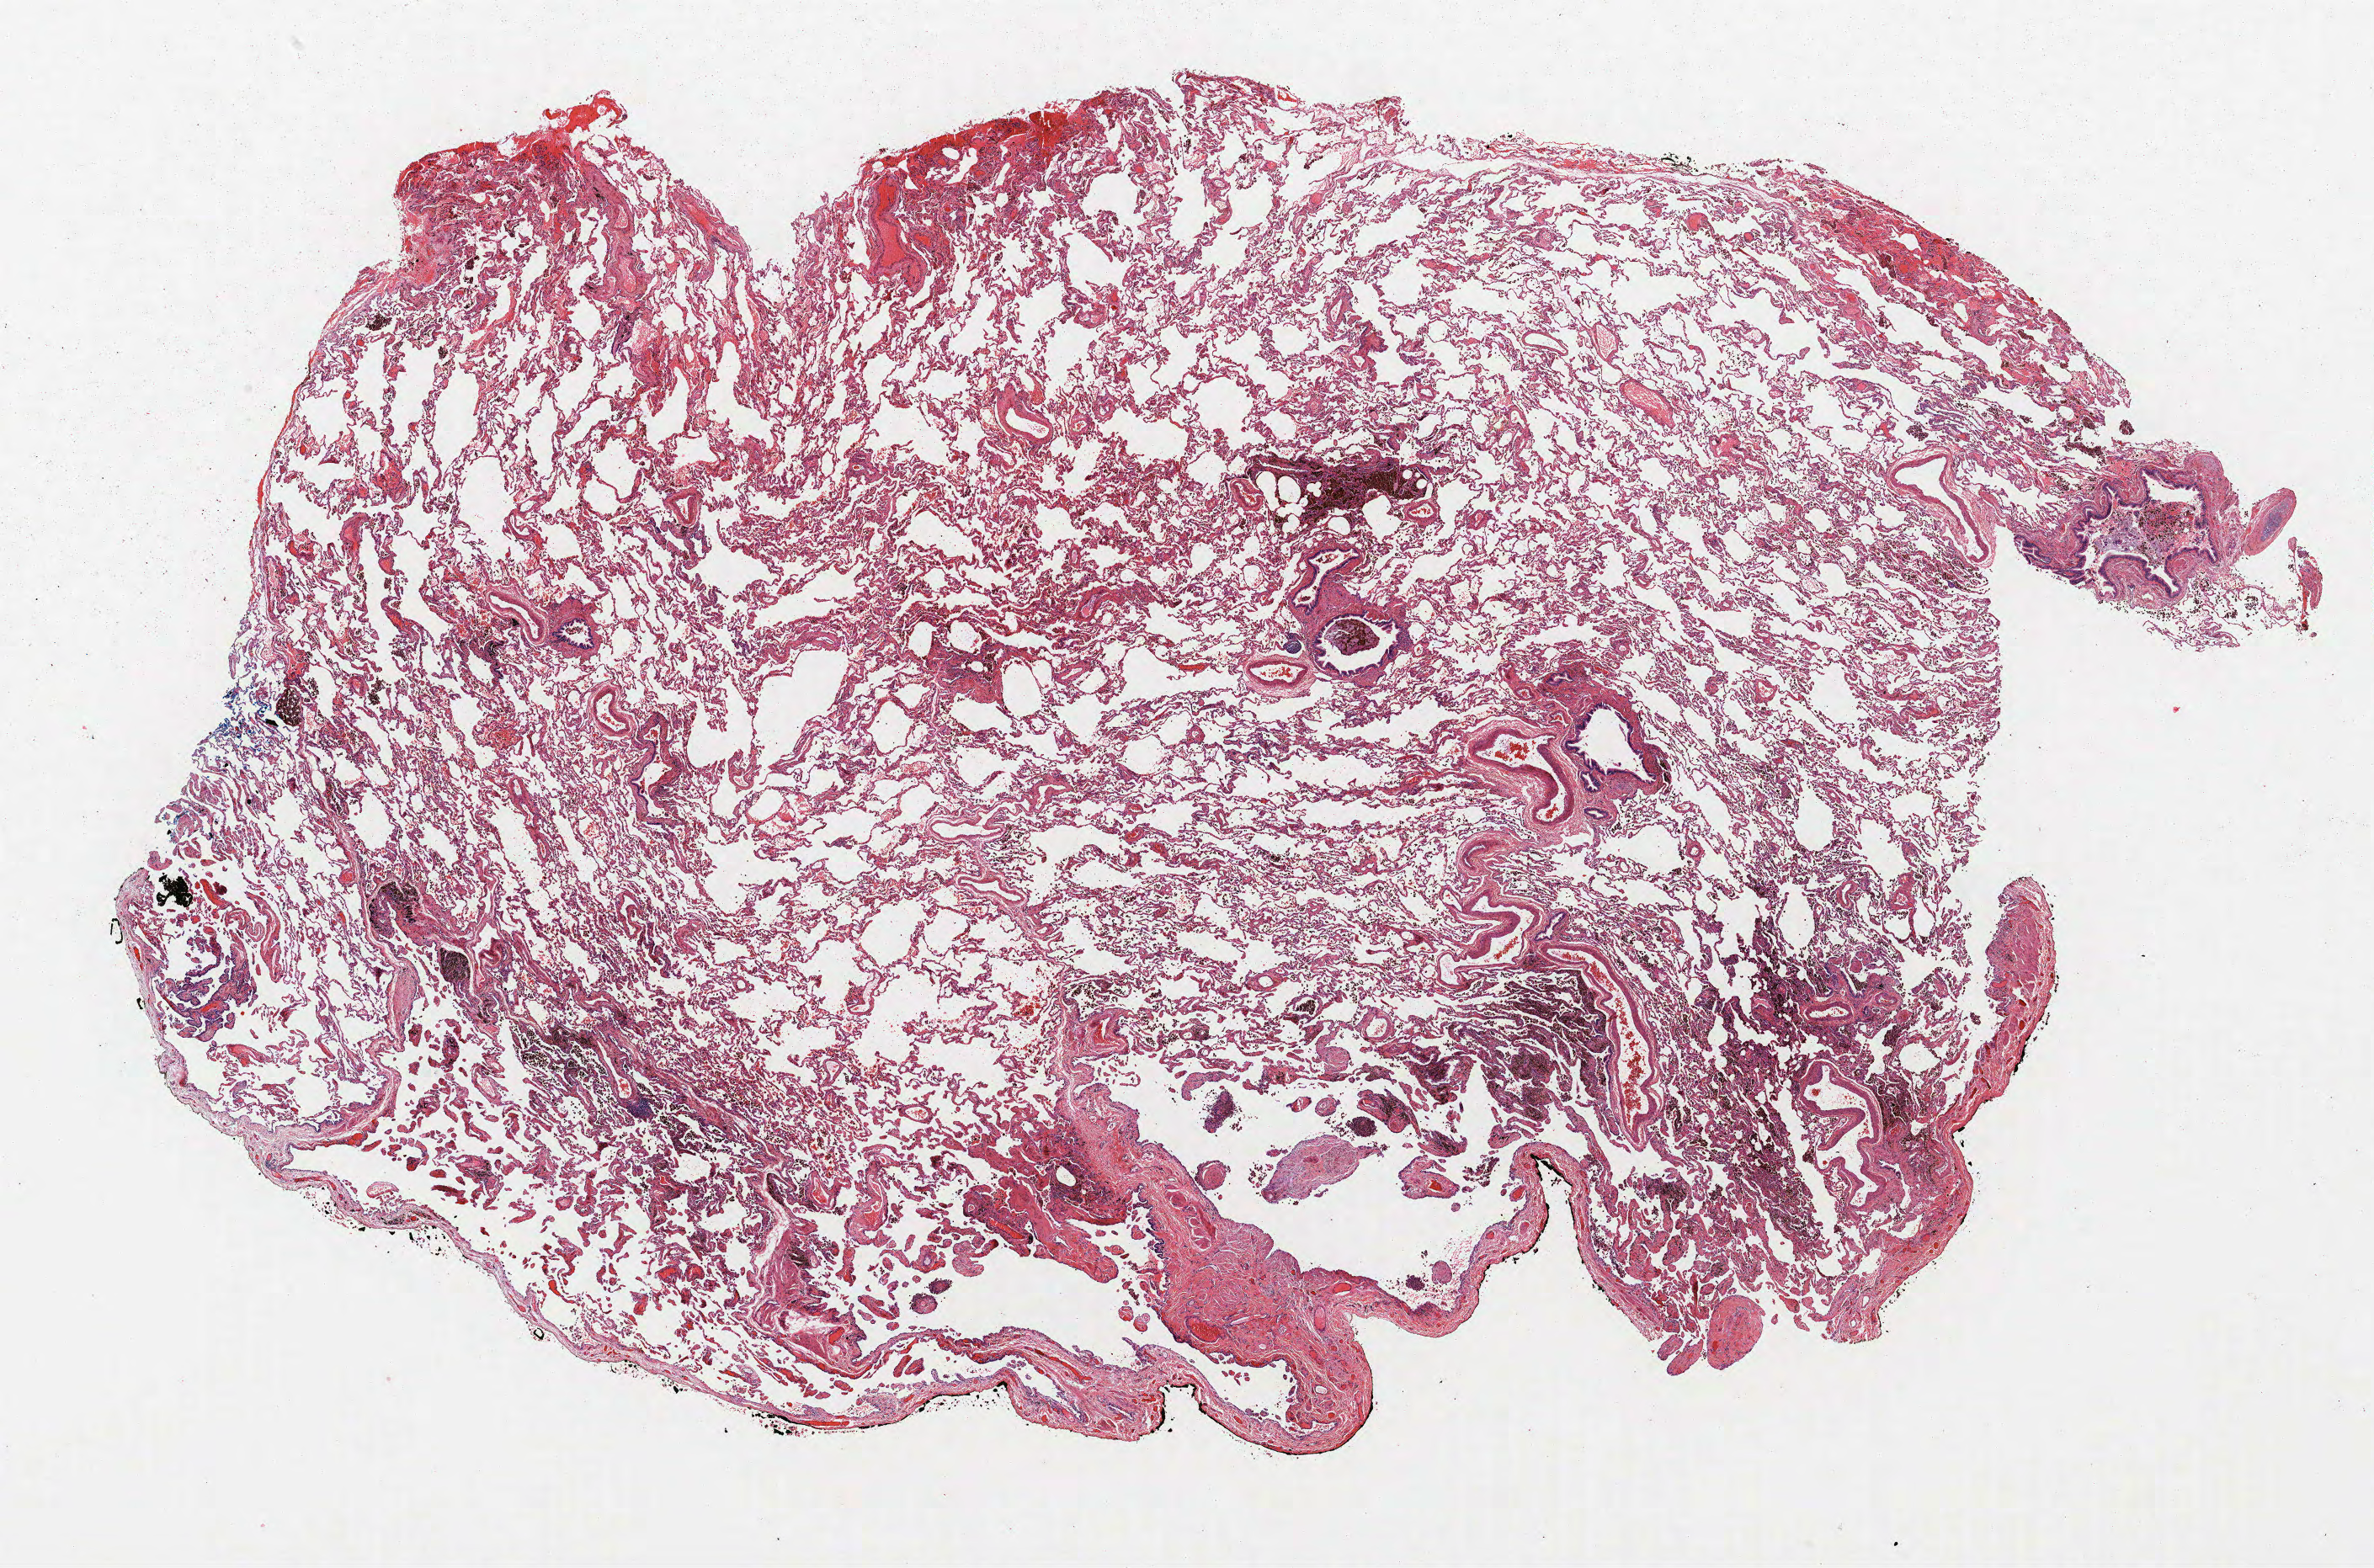
Whole-slide histology image, H&E — shown as a low-resolution overview of the whole scanned area (about 22.6 x 14.9 mm). FFPE section. Lung tissue. Male, age 60 at enrolment. Former smoker at enrolment. Grade: moderately differentiated (G2).
Stage (AJCC 6th edition): IB. Primary tumour location (clinical record): right upper lobe. Participant's lung-cancer diagnosis: Papillary adenocarcinoma, NOS. Tumour size (pathology): 32 mm.